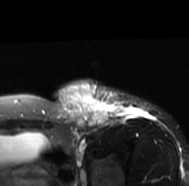
MRI of an extremity soft-tissue mass, one axial slice. Slice 57 of 77 in the series (ordered by position). T2-weighted fat-saturated. MR volume resampled by the dataset authors to the PET/CT grid (not the native acquisition matrix). 3.27 mm slice thickness. 189 × 186 image matrix, field of view 185 × 182 mm. Female patient. From the clinical record (not read from this slice): histological type: leiomyosarcoma; grade: high; site of the primary tumour: groin.
Structures marked on this image (expert contour drawn on MRI and transferred to this co-registered scan by the dataset authors):
- gross tumour volume including surrounding oedema: bounding box [x1, y1, x2, y2] px = [51, 79, 155, 128]
- gross tumour volume (mass): [56, 81, 109, 128]